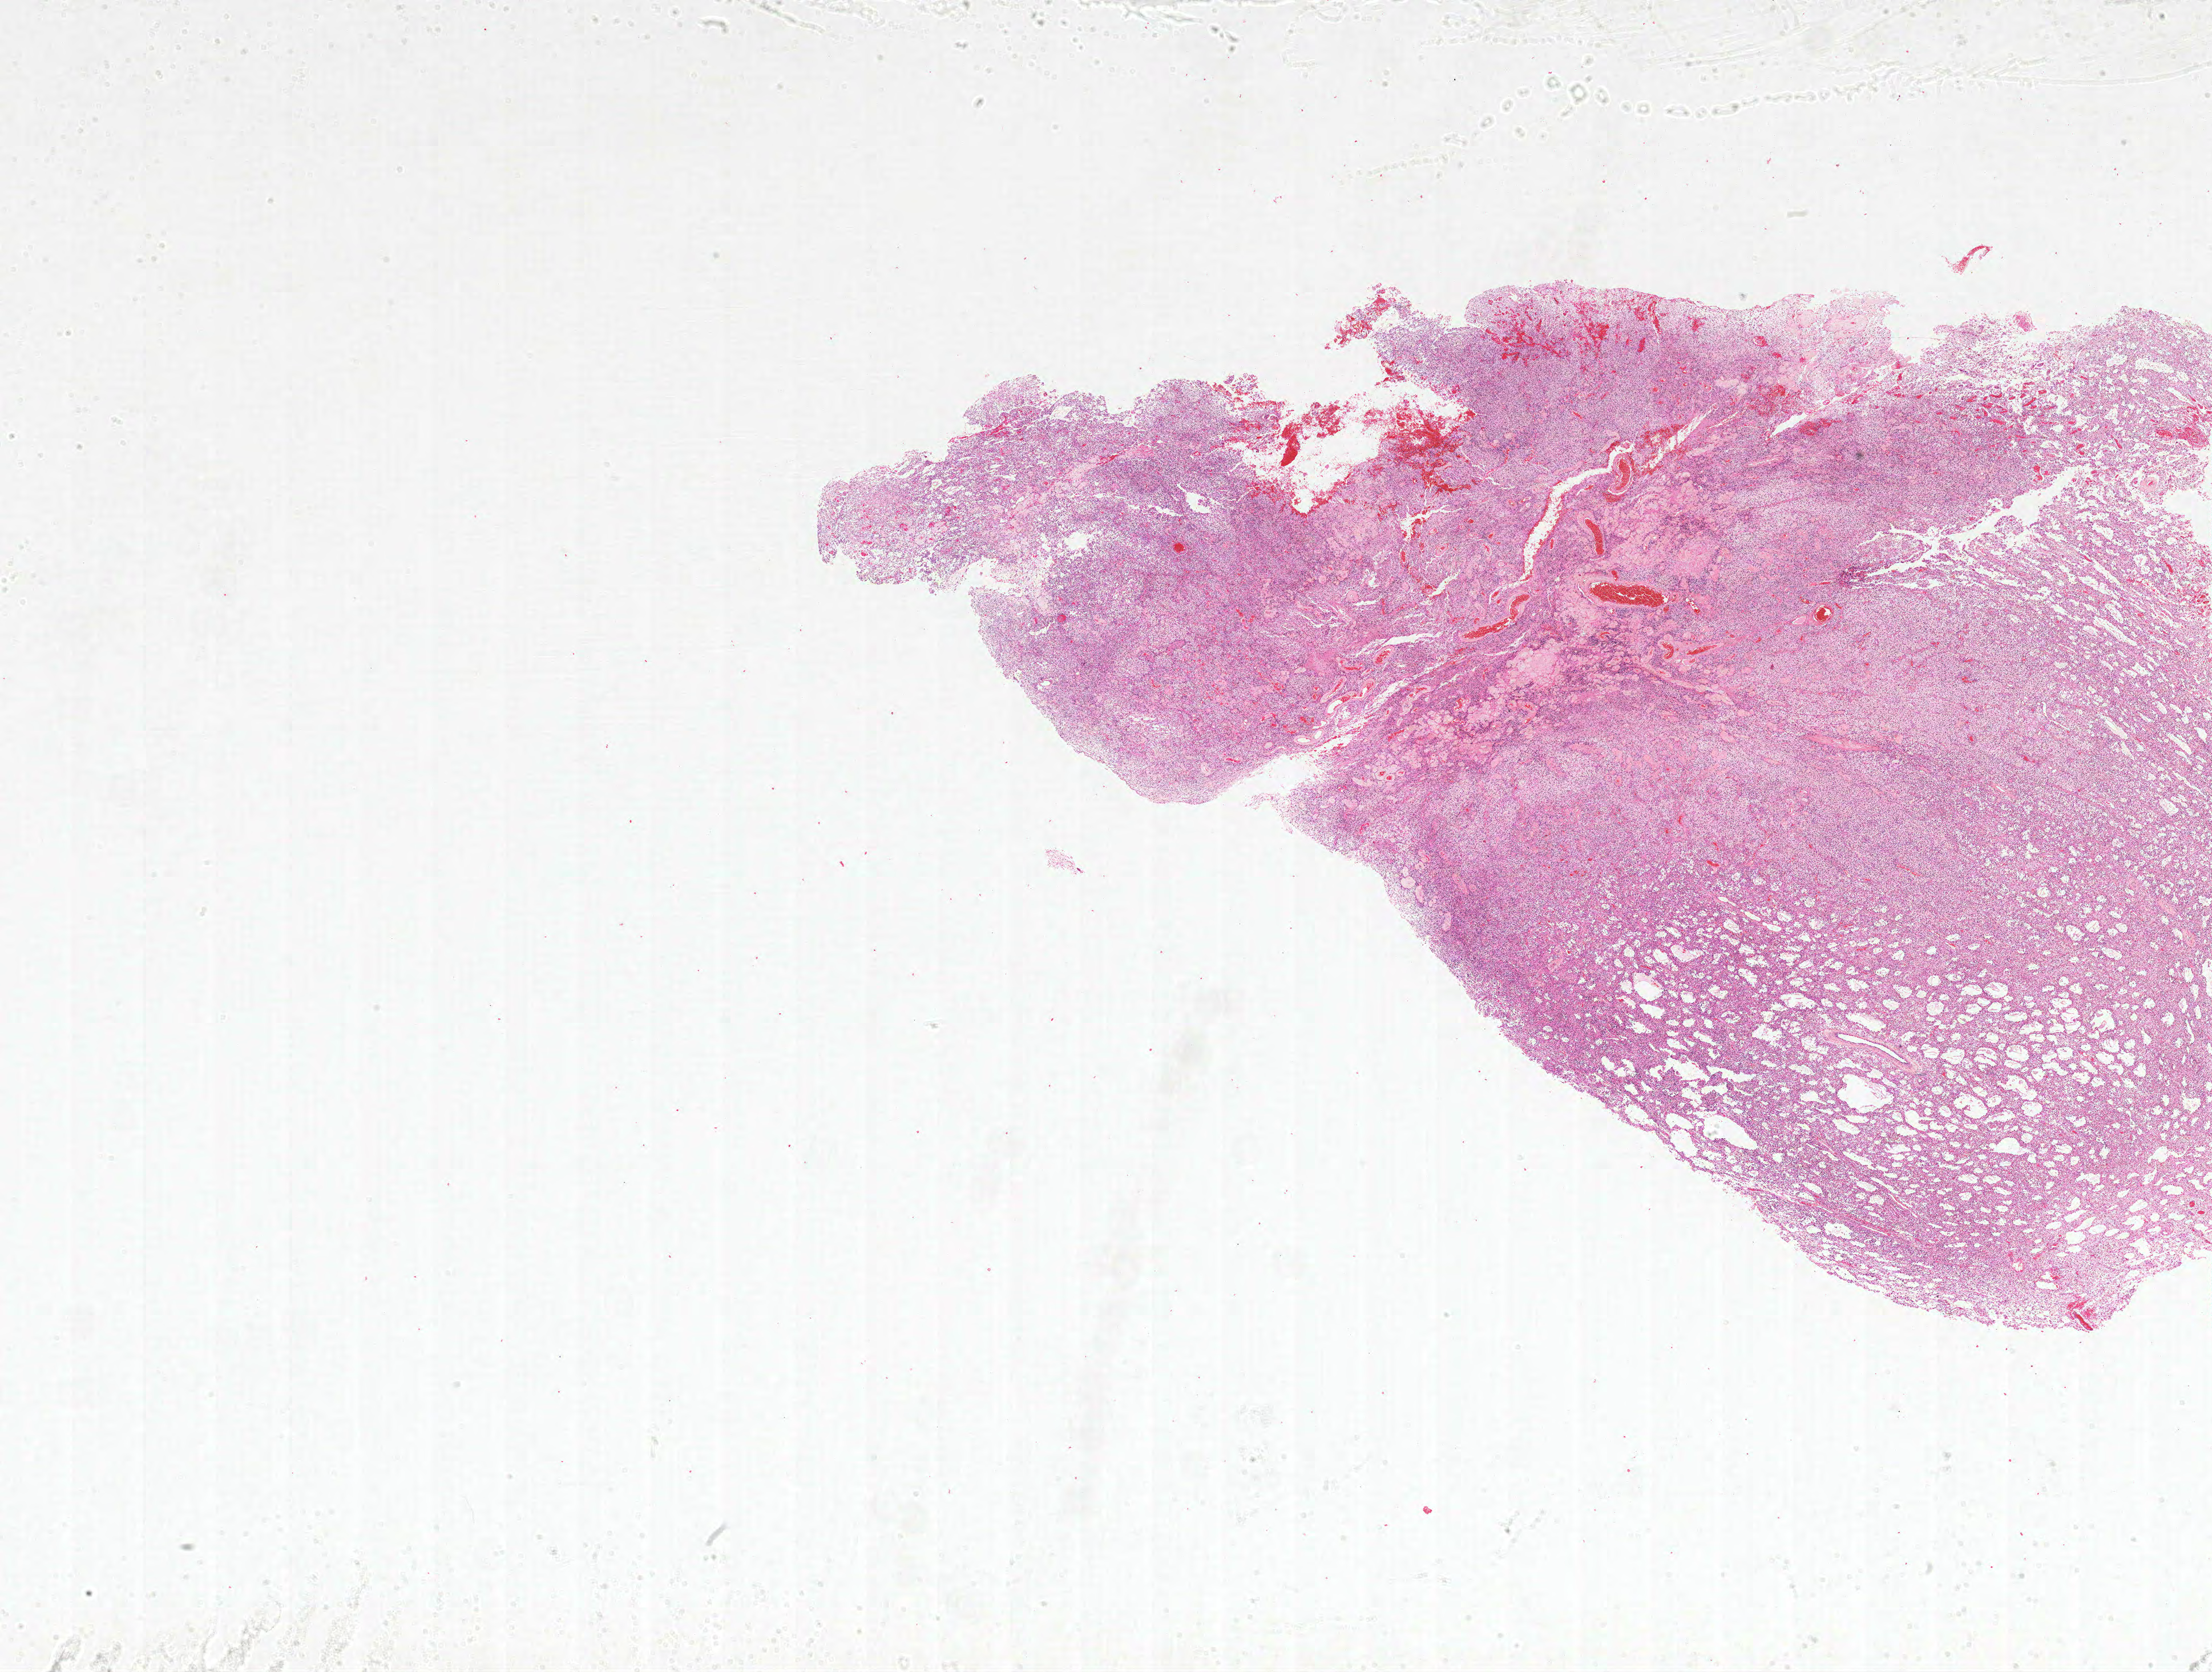
Whole-slide histology image, Hematoxylin and eosin (H&E) stained — a low-resolution overview of the entire scanned area, about 31.0 x 23.4 mm (slide scanned at 20x); formalin-fixed paraffin-embedded (FFPE) diagnostic section; primary tumour sample from the brain. Patient: female, age at initial diagnosis 45 years.
- pathologic diagnosis: Glioblastoma